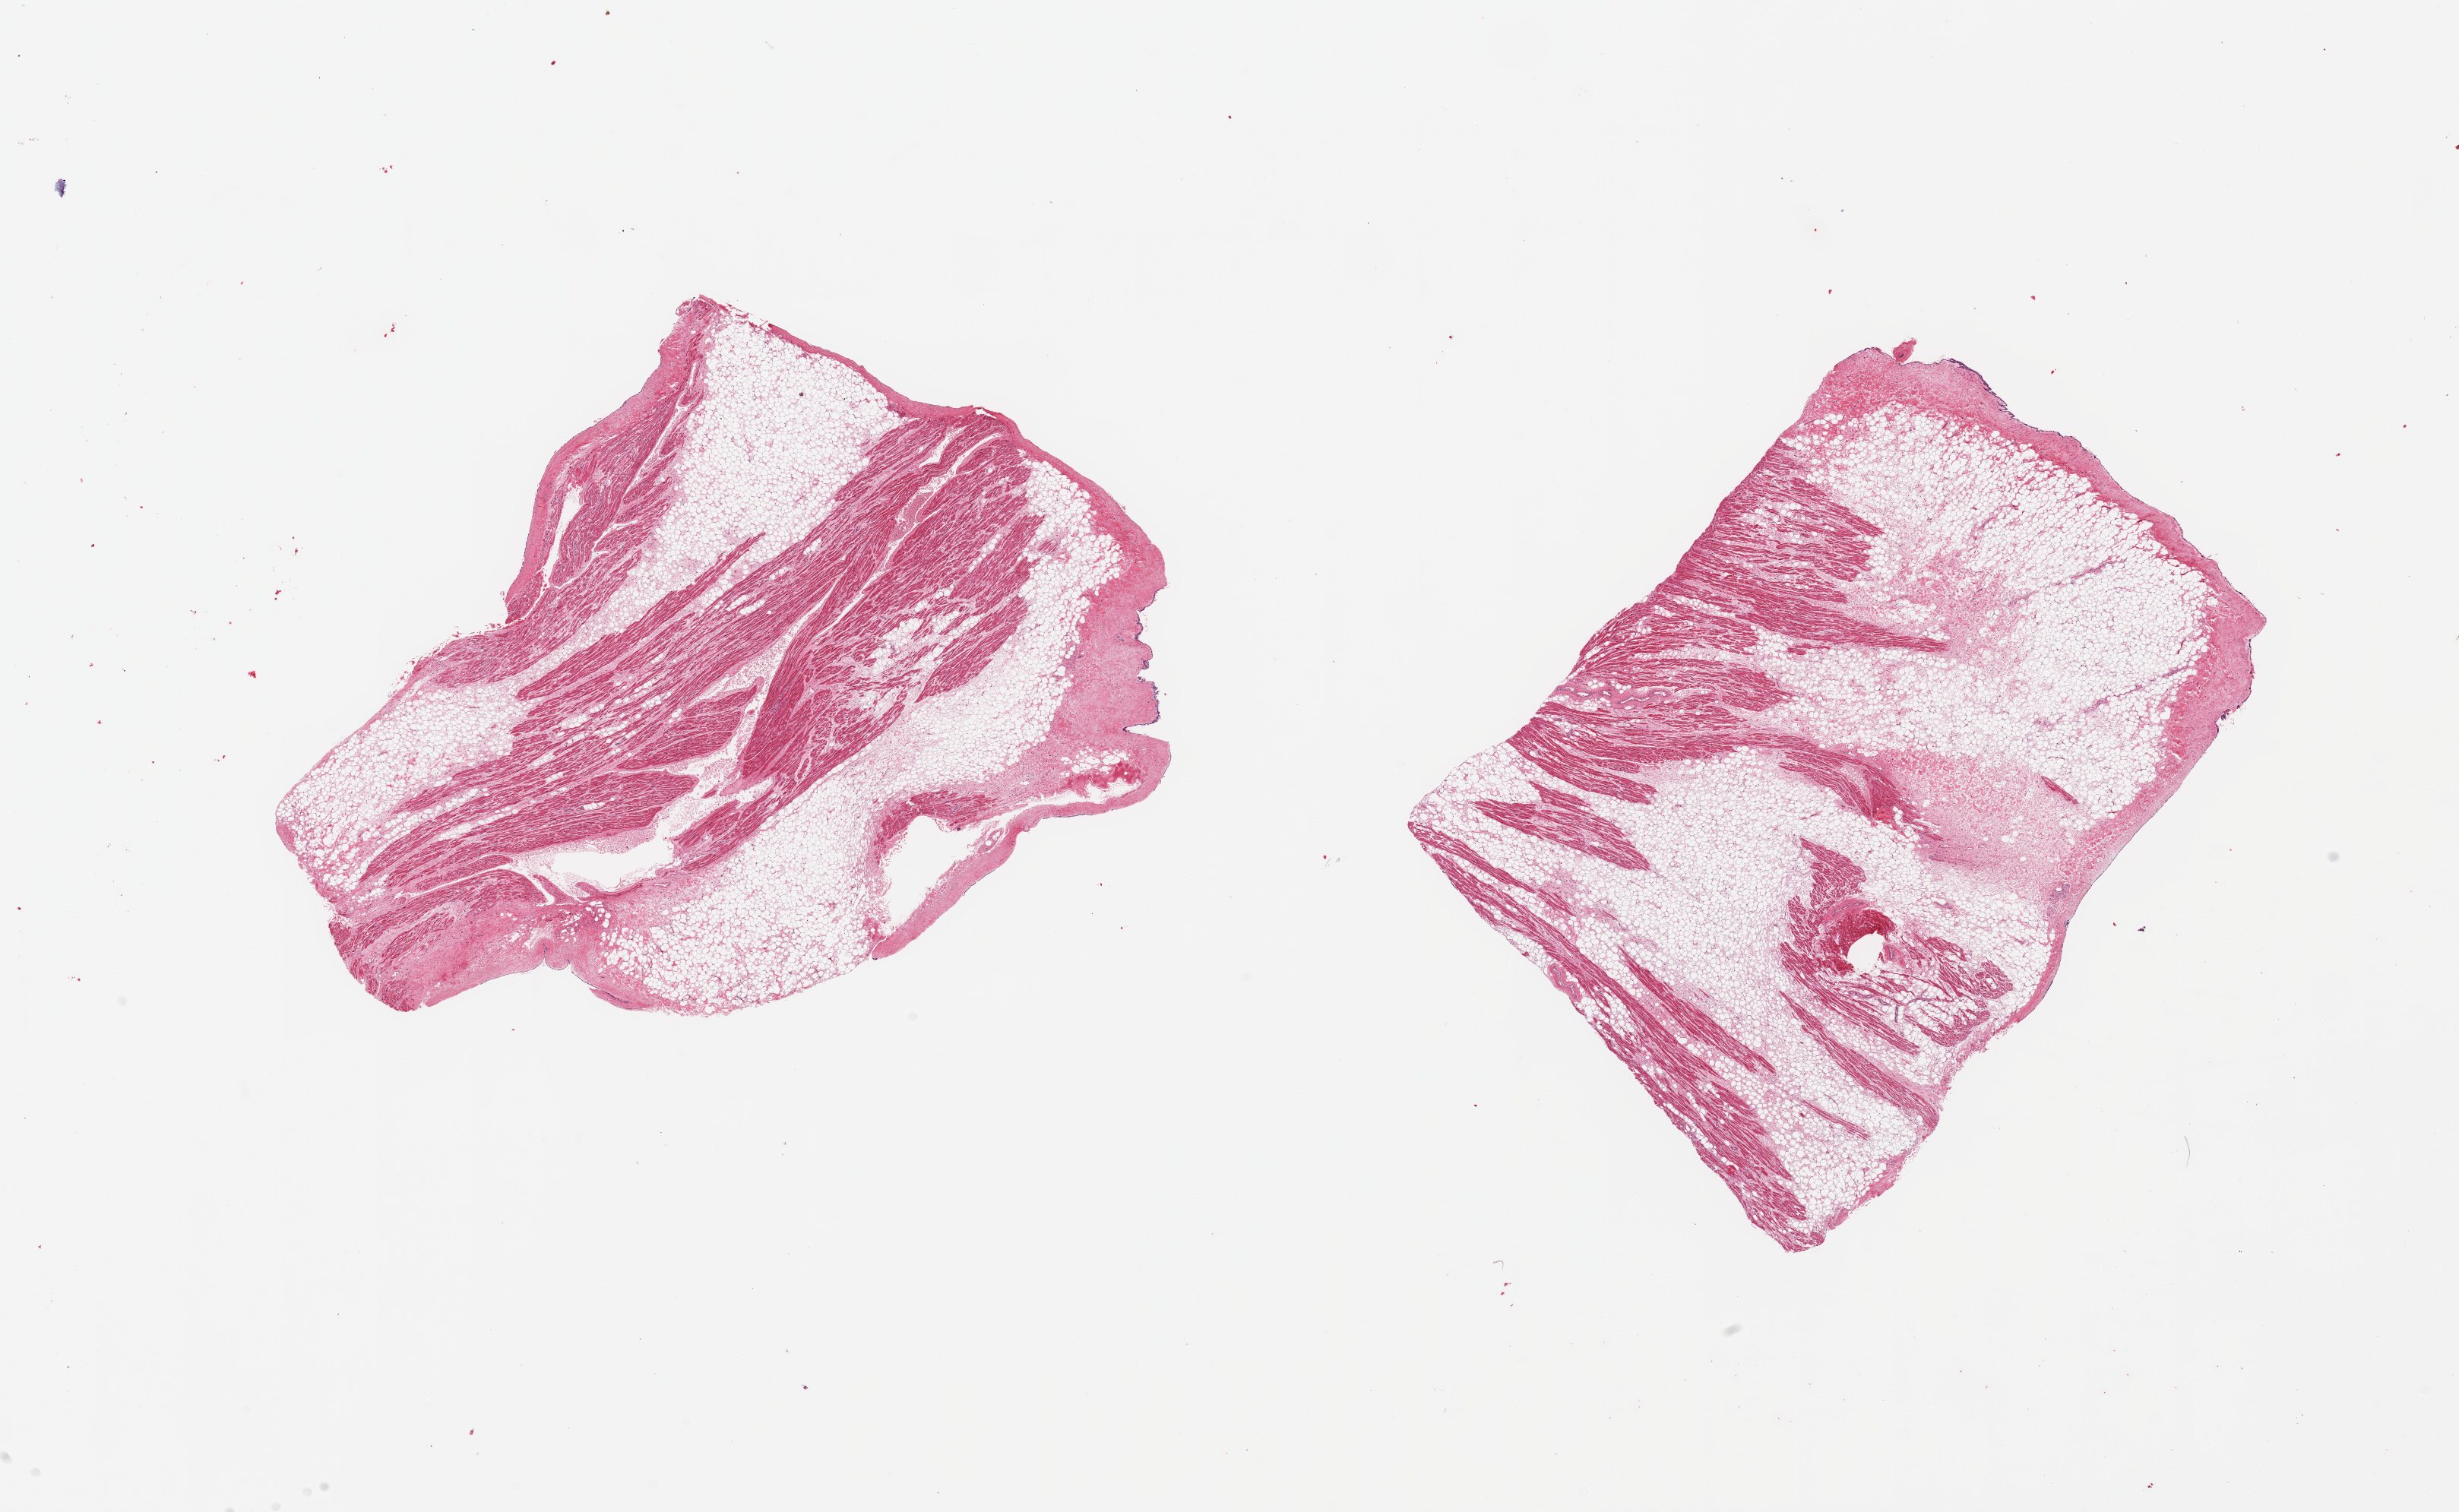
Haematoxylin and eosin whole-slide image, brightfield, whole scanned area (about 25.6 x 15.7 mm, from a 20x scan) shown as a low-resolution overview, PAXgene-fixed, paraffin-embedded tissue, target tissue: auricular appendage, tissue donor sample. Donor: male.
Pathologist's review note for this sample: 2 pieces; 60% & 40% internal fat.